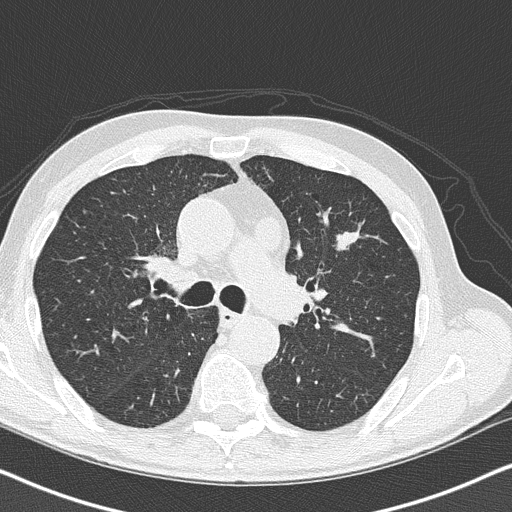
Low-dose screening chest CT, one axial slice. Position 103 of 158 along the scan axis. Reconstruction kernel B50f. Lung window (W 1500 / L -600 HU). 512 × 512 image matrix, field of view 330 × 330 mm.
Outlined on this slice (manually delineated by an expert):
- lesion 1 (tumor, upper lobe of left lung): bounding box <337,232,359,250> (left, top, right, bottom; pixels)